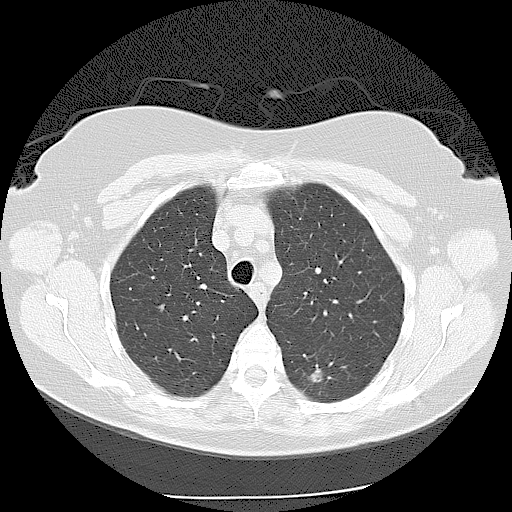
Low-dose screening chest CT, one axial slice. Position 87 of 116 along the scan axis. Reconstruction kernel LUNG. 120 kVp. Lung window (W 1500 / L -600 HU). 2.5 mm slice thickness. 512 × 512 image matrix, field of view 360 × 360 mm.
Annotated regions visible in this slice (expert manual segmentation):
- lesion 1 (tumor, lower lobe of left lung): bounding box (x1, y1, x2, y2) in pixels: (308, 368, 322, 383)